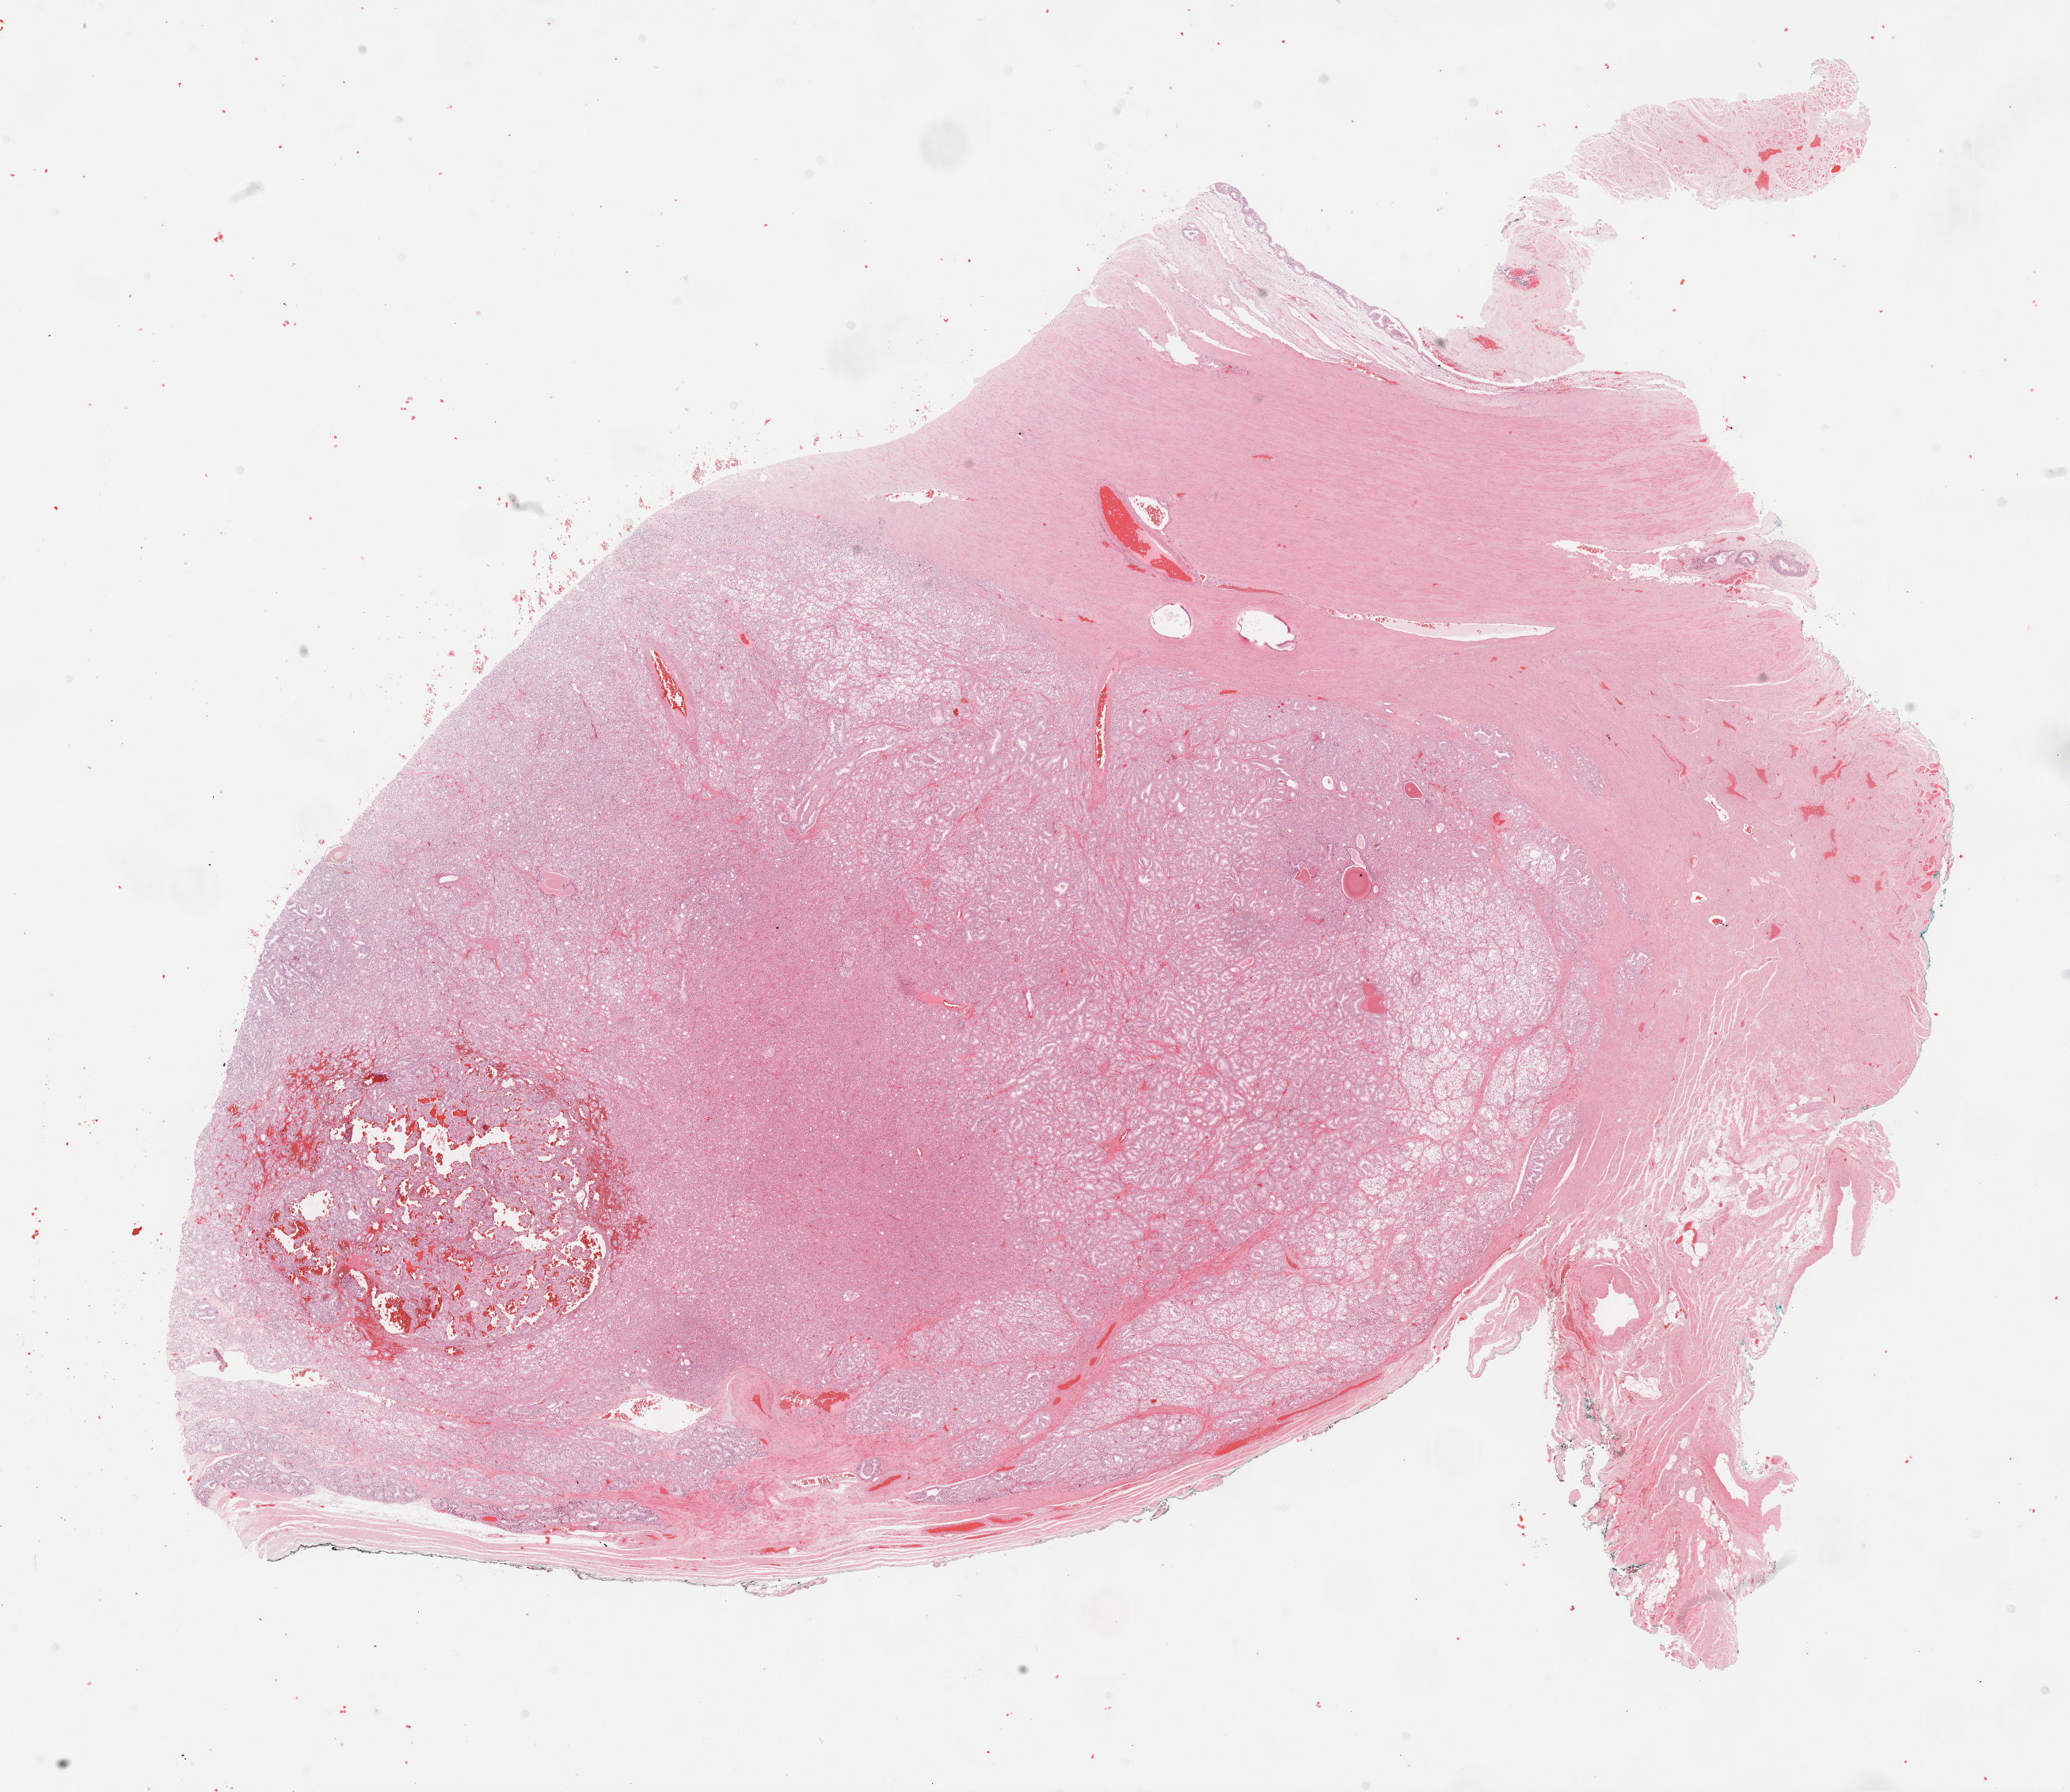
Hematoxylin and eosin (H&E) stained whole-slide image — shown as a low-resolution overview of the whole scanned area (about 21.1 x 18.3 mm), formalin-fixed paraffin-embedded (FFPE) diagnostic section, prostate, primary tumour sample. Patient: male, age at initial diagnosis 72 years. Gleason score: 8 (4+4).
Lymph nodes positive (case pathology): 0 of 4 examined. Pathologic diagnosis: Adenocarcinoma, NOS (prostate gland).